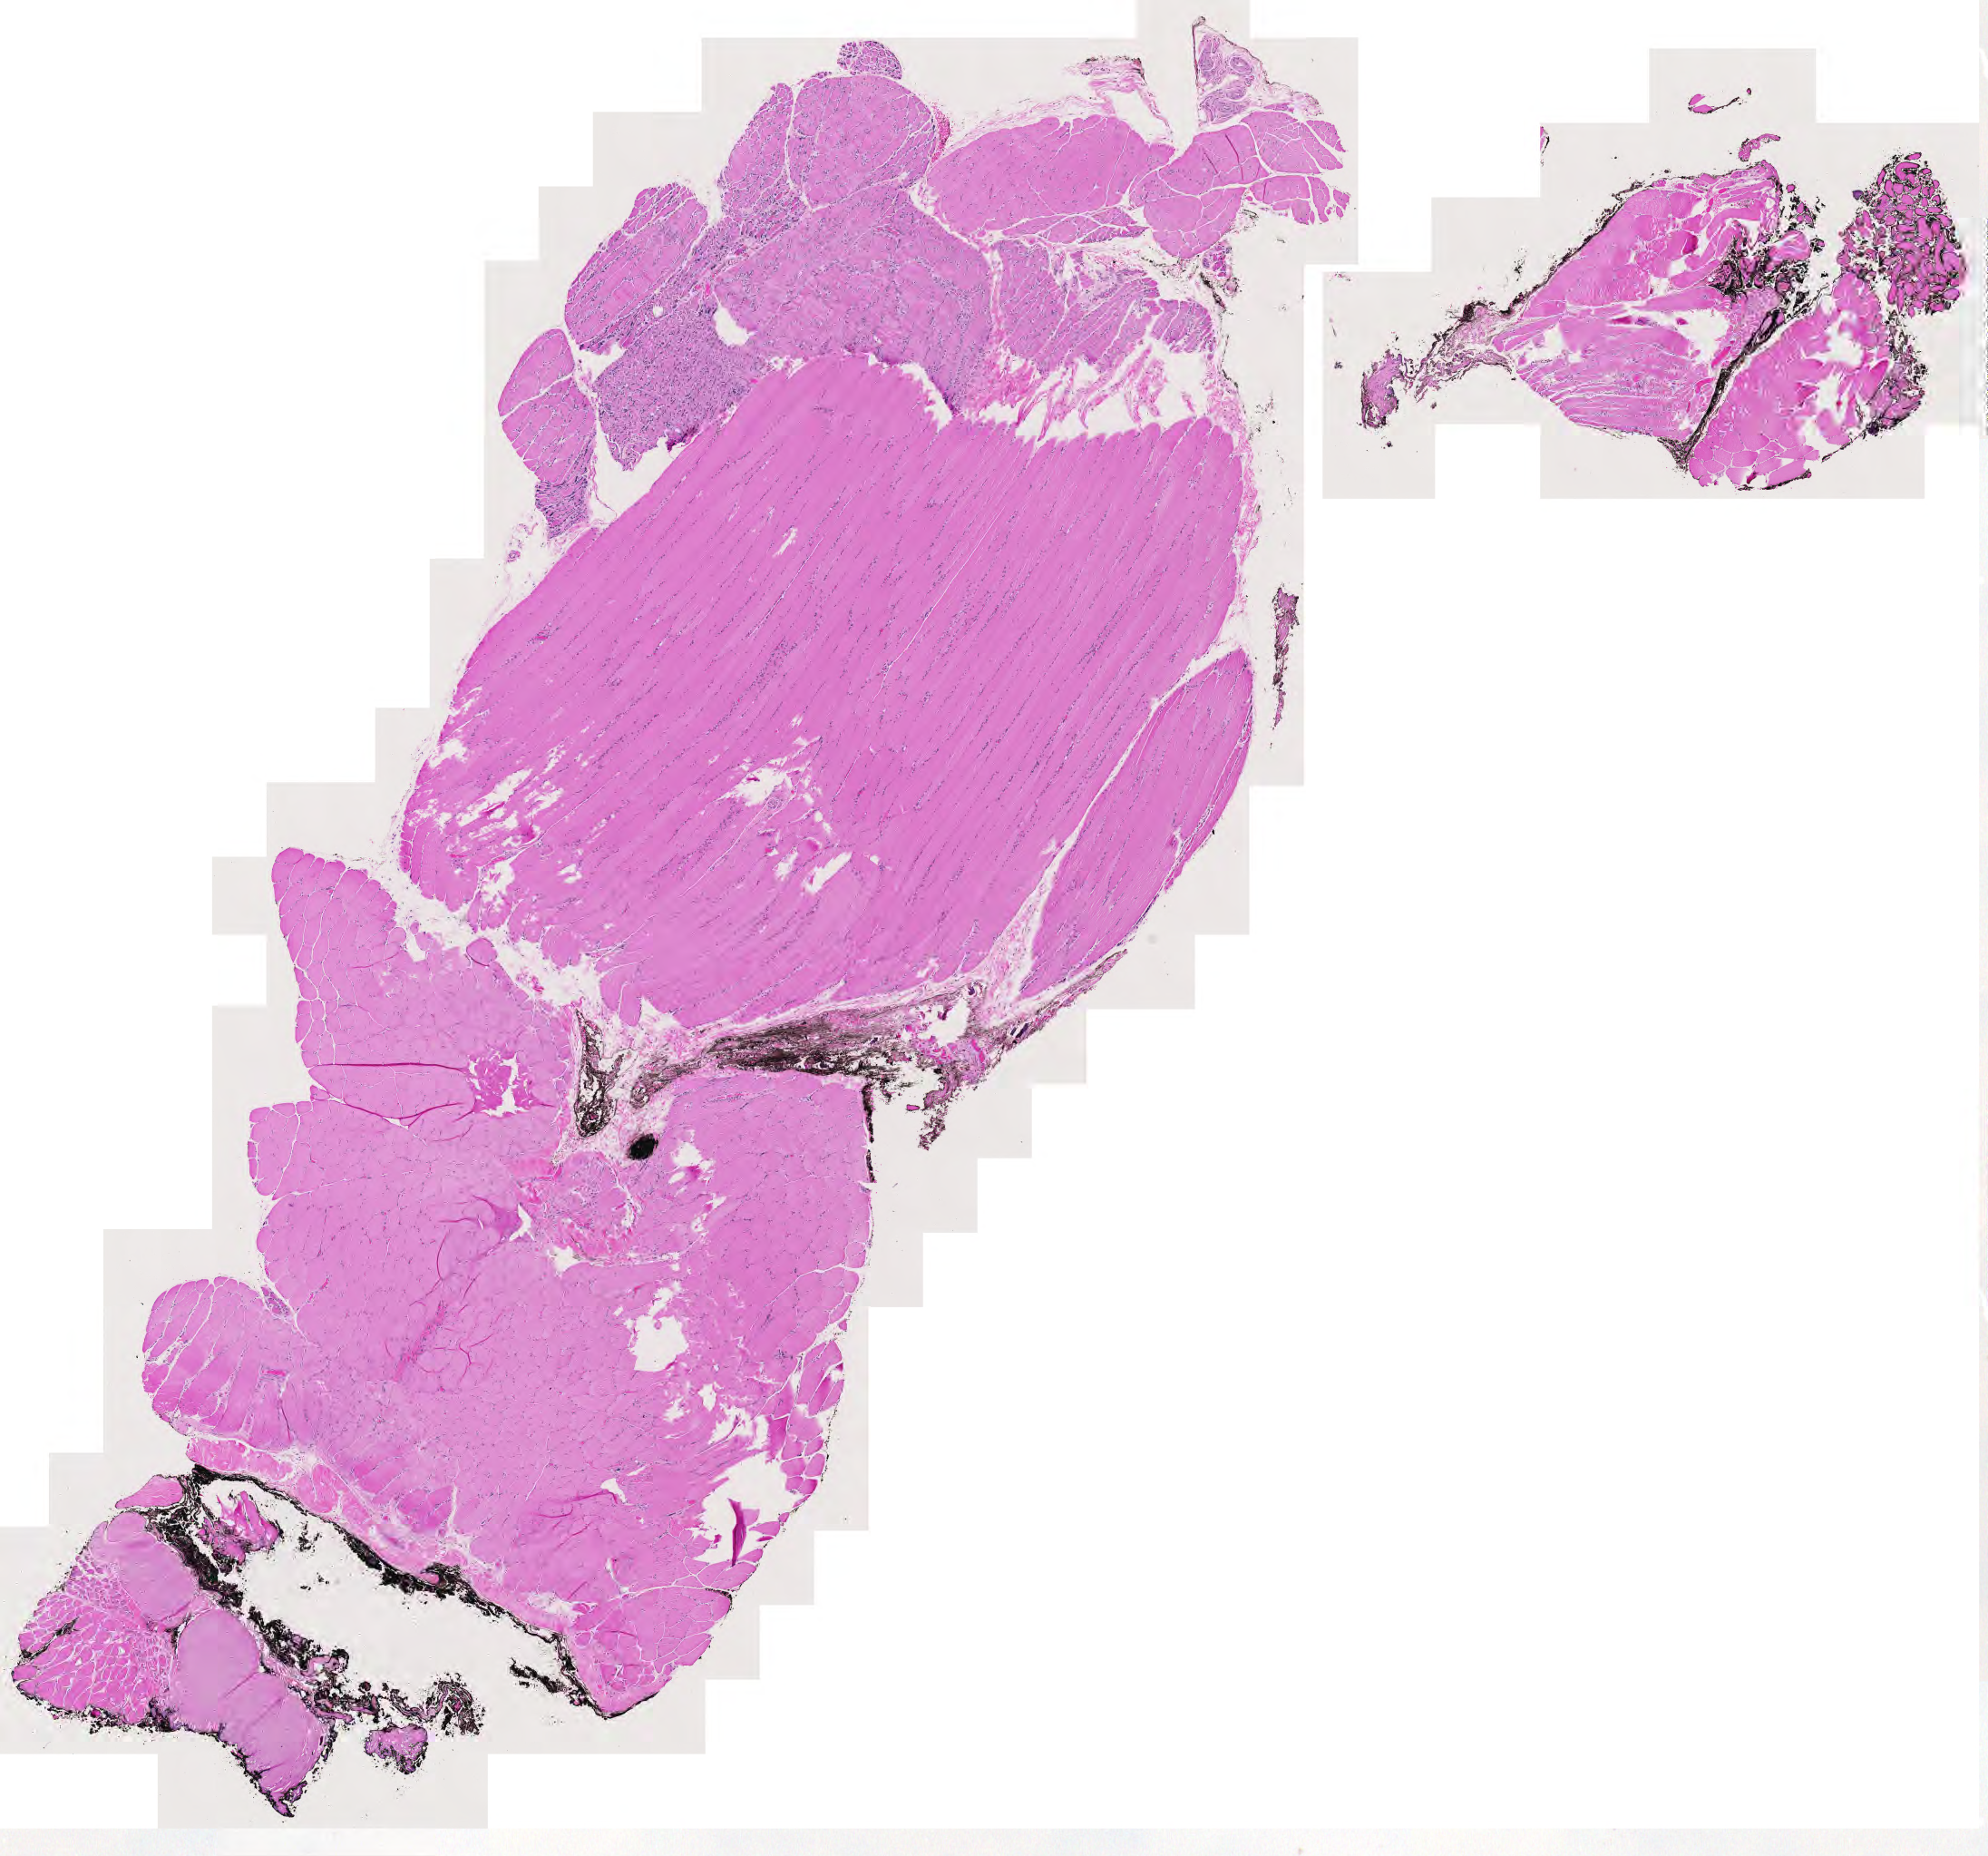
Digitized Hematoxylin and eosin (H&E) stained tissue section (whole slide), low-resolution overview of the scanned area, about 11.3 x 10.6 mm (from a 20x scan). Normal (non-tumour) tissue sample. 49-year-old male patient.
* this section: normal (non-tumour) tissue from the same patient
* patient diagnosis (cohort enrolment): sarcoma (site not recorded at cohort level)